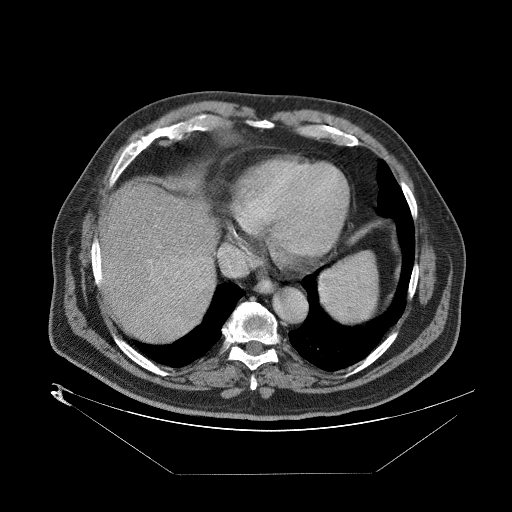
Contrast-enhanced abdominal CT (liver protocol), one axial slice. Slice 74 of 89 in the series (ordered by position). One of 2 acquisitions stored at this slice position. Soft-tissue window (W 400 / L 40 HU). 2.5 mm slice thickness. 512 × 512 image matrix, field of view 480 × 480 mm. Case-level facts recorded for this patient, not image findings: diagnosis: hepatocellular carcinoma (patient treated with transarterial chemoembolisation; whether this scan precedes or follows treatment is not stated here); TNM stage (as recorded): Stage-II; Child-Pugh class: B; tumour nodularity: multinodular.
Outlined on this slice (semi-automatically segmented with operator editing):
- abdominal aorta: bounding box (x1, y1, x2, y2) in pixels: (272, 287, 307, 322)
- liver parenchyma outside the tumour (the mass and vessels are separate outlines, so this box may not span the whole liver): (96, 178, 219, 336)
- mass: (147, 250, 212, 323)